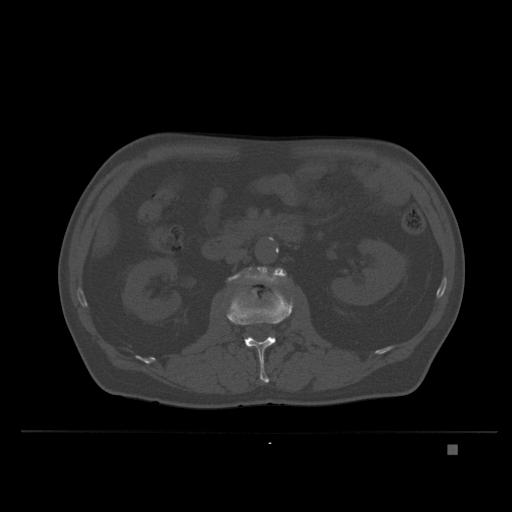
CT including the spine, one axial slice. Slice 113 of 435 in the series (ordered by position). Bone window (W 1800 / L 400 HU). 512 × 512 image matrix, field of view 434 × 434 mm. Patient: male, 73 years. Case-level facts recorded for this patient, not image findings: primary cancer: skin.
Outlined on this slice (semi-automatic segmentation, software-assisted and operator-edited):
- L2 vertebra: bounding box [x1, y1, x2, y2] px = [226, 288, 294, 383]
- L3 vertebra: [228, 267, 287, 282]